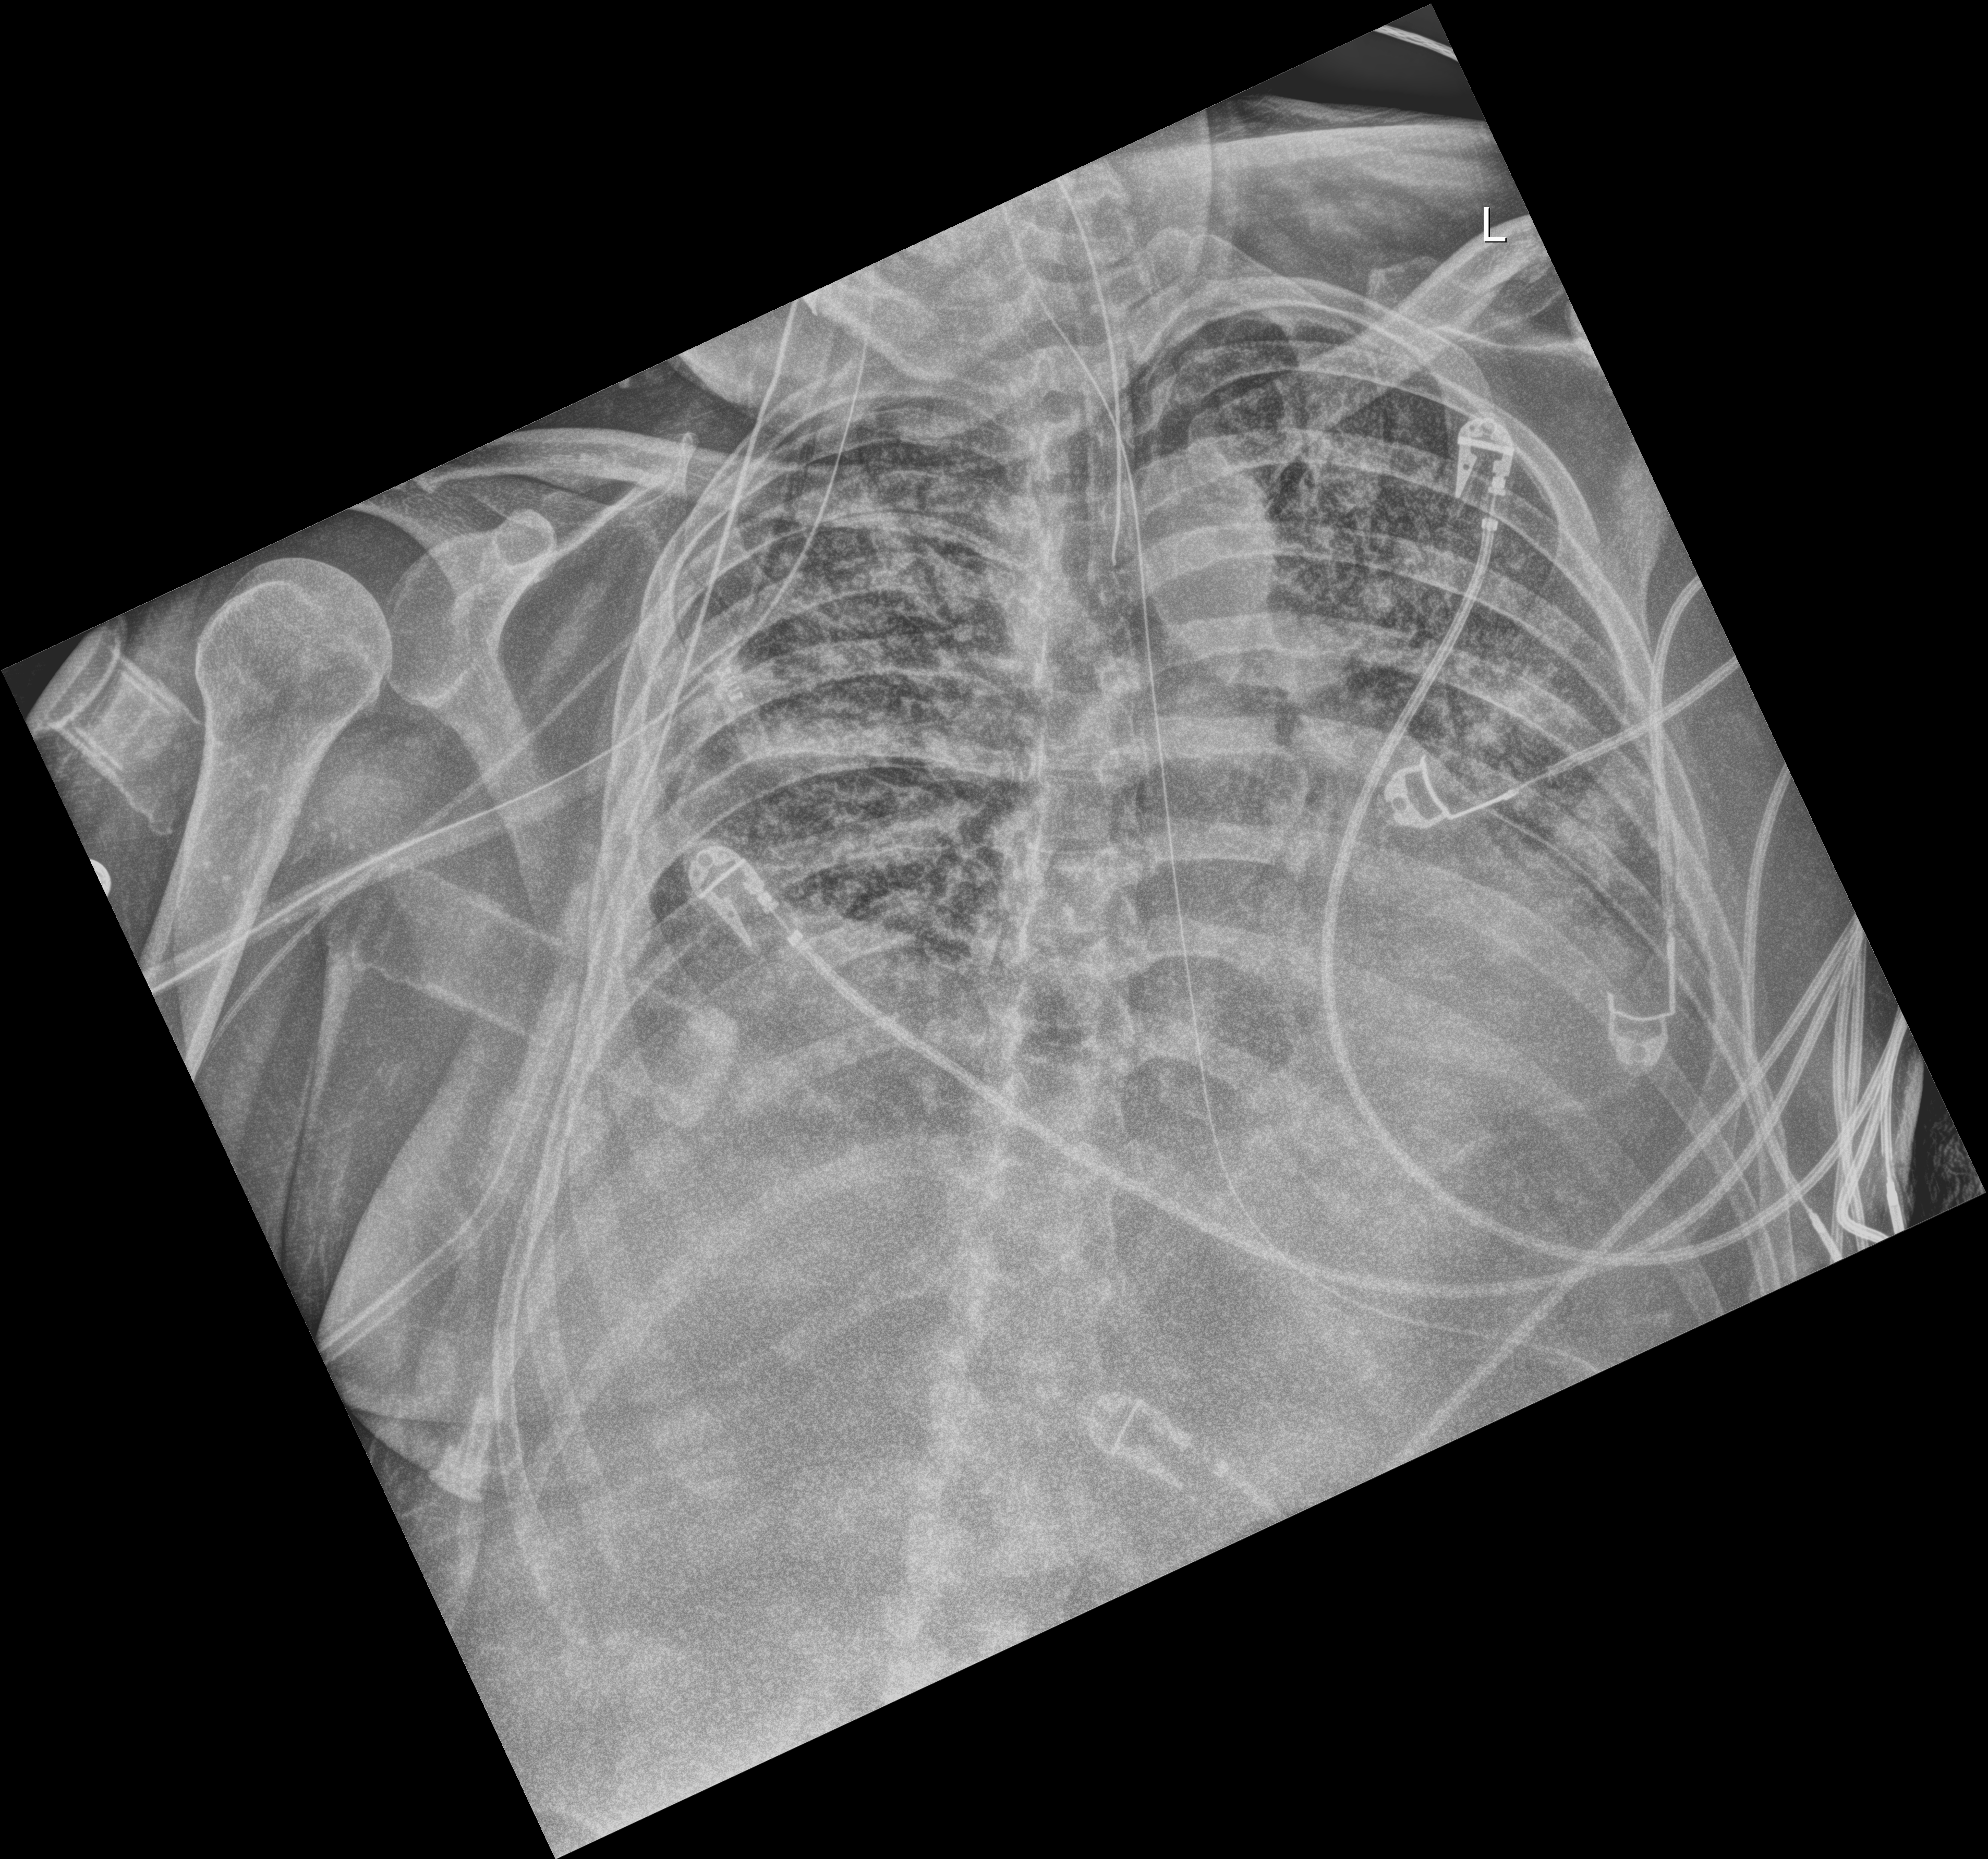
Portable chest radiograph, anteroposterior (AP) projection. Patient hospitalised with COVID-19; male, aged 18–59 years.
From the hospital-stay record, not from the radiograph (when in the stay this image was taken is not recorded): chronic kidney disease (admission record): no; hypertension (admission record): no; mechanically ventilated during this hospital stay: yes.